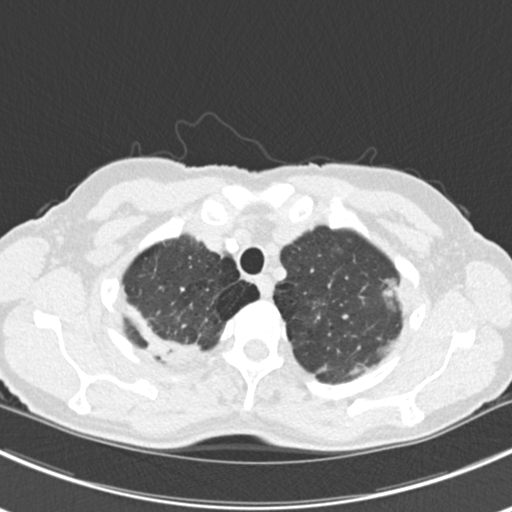
Chest CT (low-dose screening protocol), one axial image, first (baseline) screen, lung window (W 1500 / L -600 HU), standard (soft-tissue) reconstruction kernel (B30f), slice 30 of 224 in the series. Female participant, aged 63 years at enrolment. Current smoker at enrolment.
Expert-annotated lung lesion, bounding box (x1, y1, x2, y2) in pixels: (366, 269, 418, 321). The screening reader recorded 10 non-calcified nodules or masses ≥4 mm on this exam (right lower lobe, right lower lobe, left lower lobe, left lower lobe, right middle lobe, right lower lobe, left lower lobe, left upper lobe, right upper lobe, left upper lobe); which of them this box marks is not recorded. Official screen result: positive, change unspecified: nodule(s) >= 4 mm or enlarging nodule(s), mass(es), or other non-specific abnormalities suspicious for lung cancer. Participant outcome: lung cancer diagnosed 751 days after this screen (after the third annual screen) — bronchiolo-alveolar adenocarcinoma, NOS, right upper lobe, right middle lobe, right lower lobe, left upper lobe, left lower lobe, moderately differentiated (G2), stage IV (AJCC 6th edition).